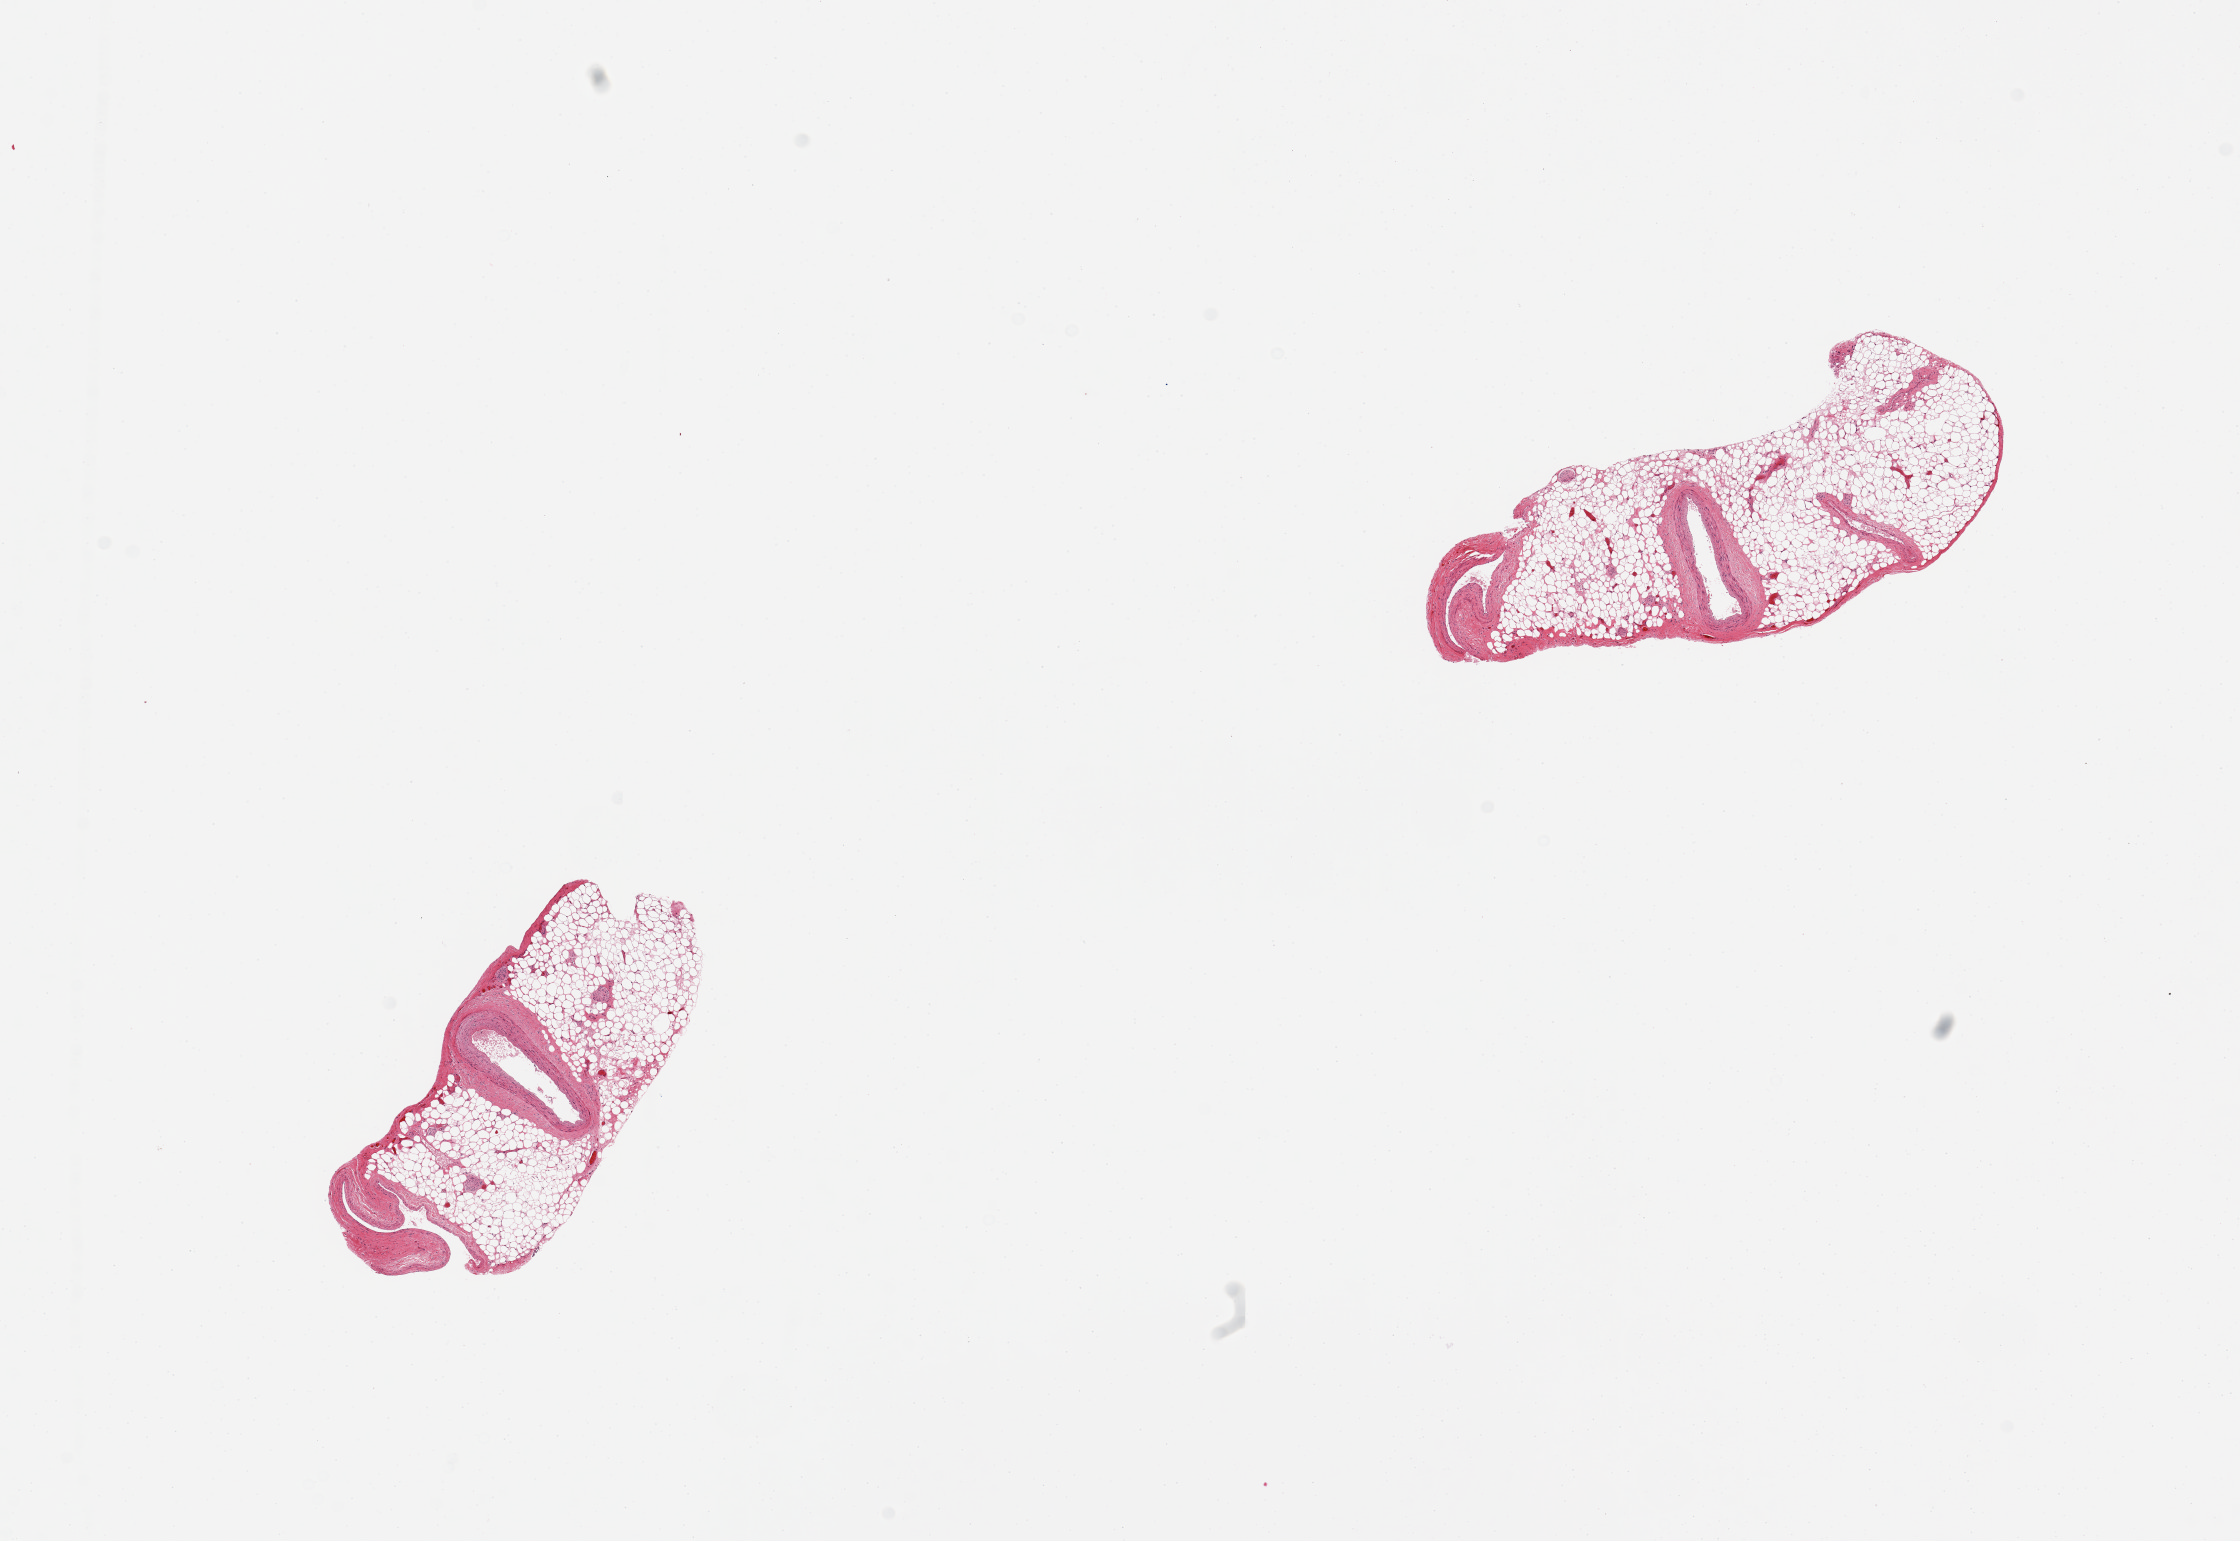
Digitized hematoxylin and eosin (H&E)-stained section, brightfield — shown as a low-resolution overview of the whole scanned area (about 17.7 x 12.2 mm); PAXgene-fixed paraffin-embedded (PFPE) section; section of coronary artery (target tissue); donor tissue sample.
Reviewer comment on this tissue sample: 2 pieces both ~70% adherent 2mm nubbins of fat, small (~1x0.5mm vessels).